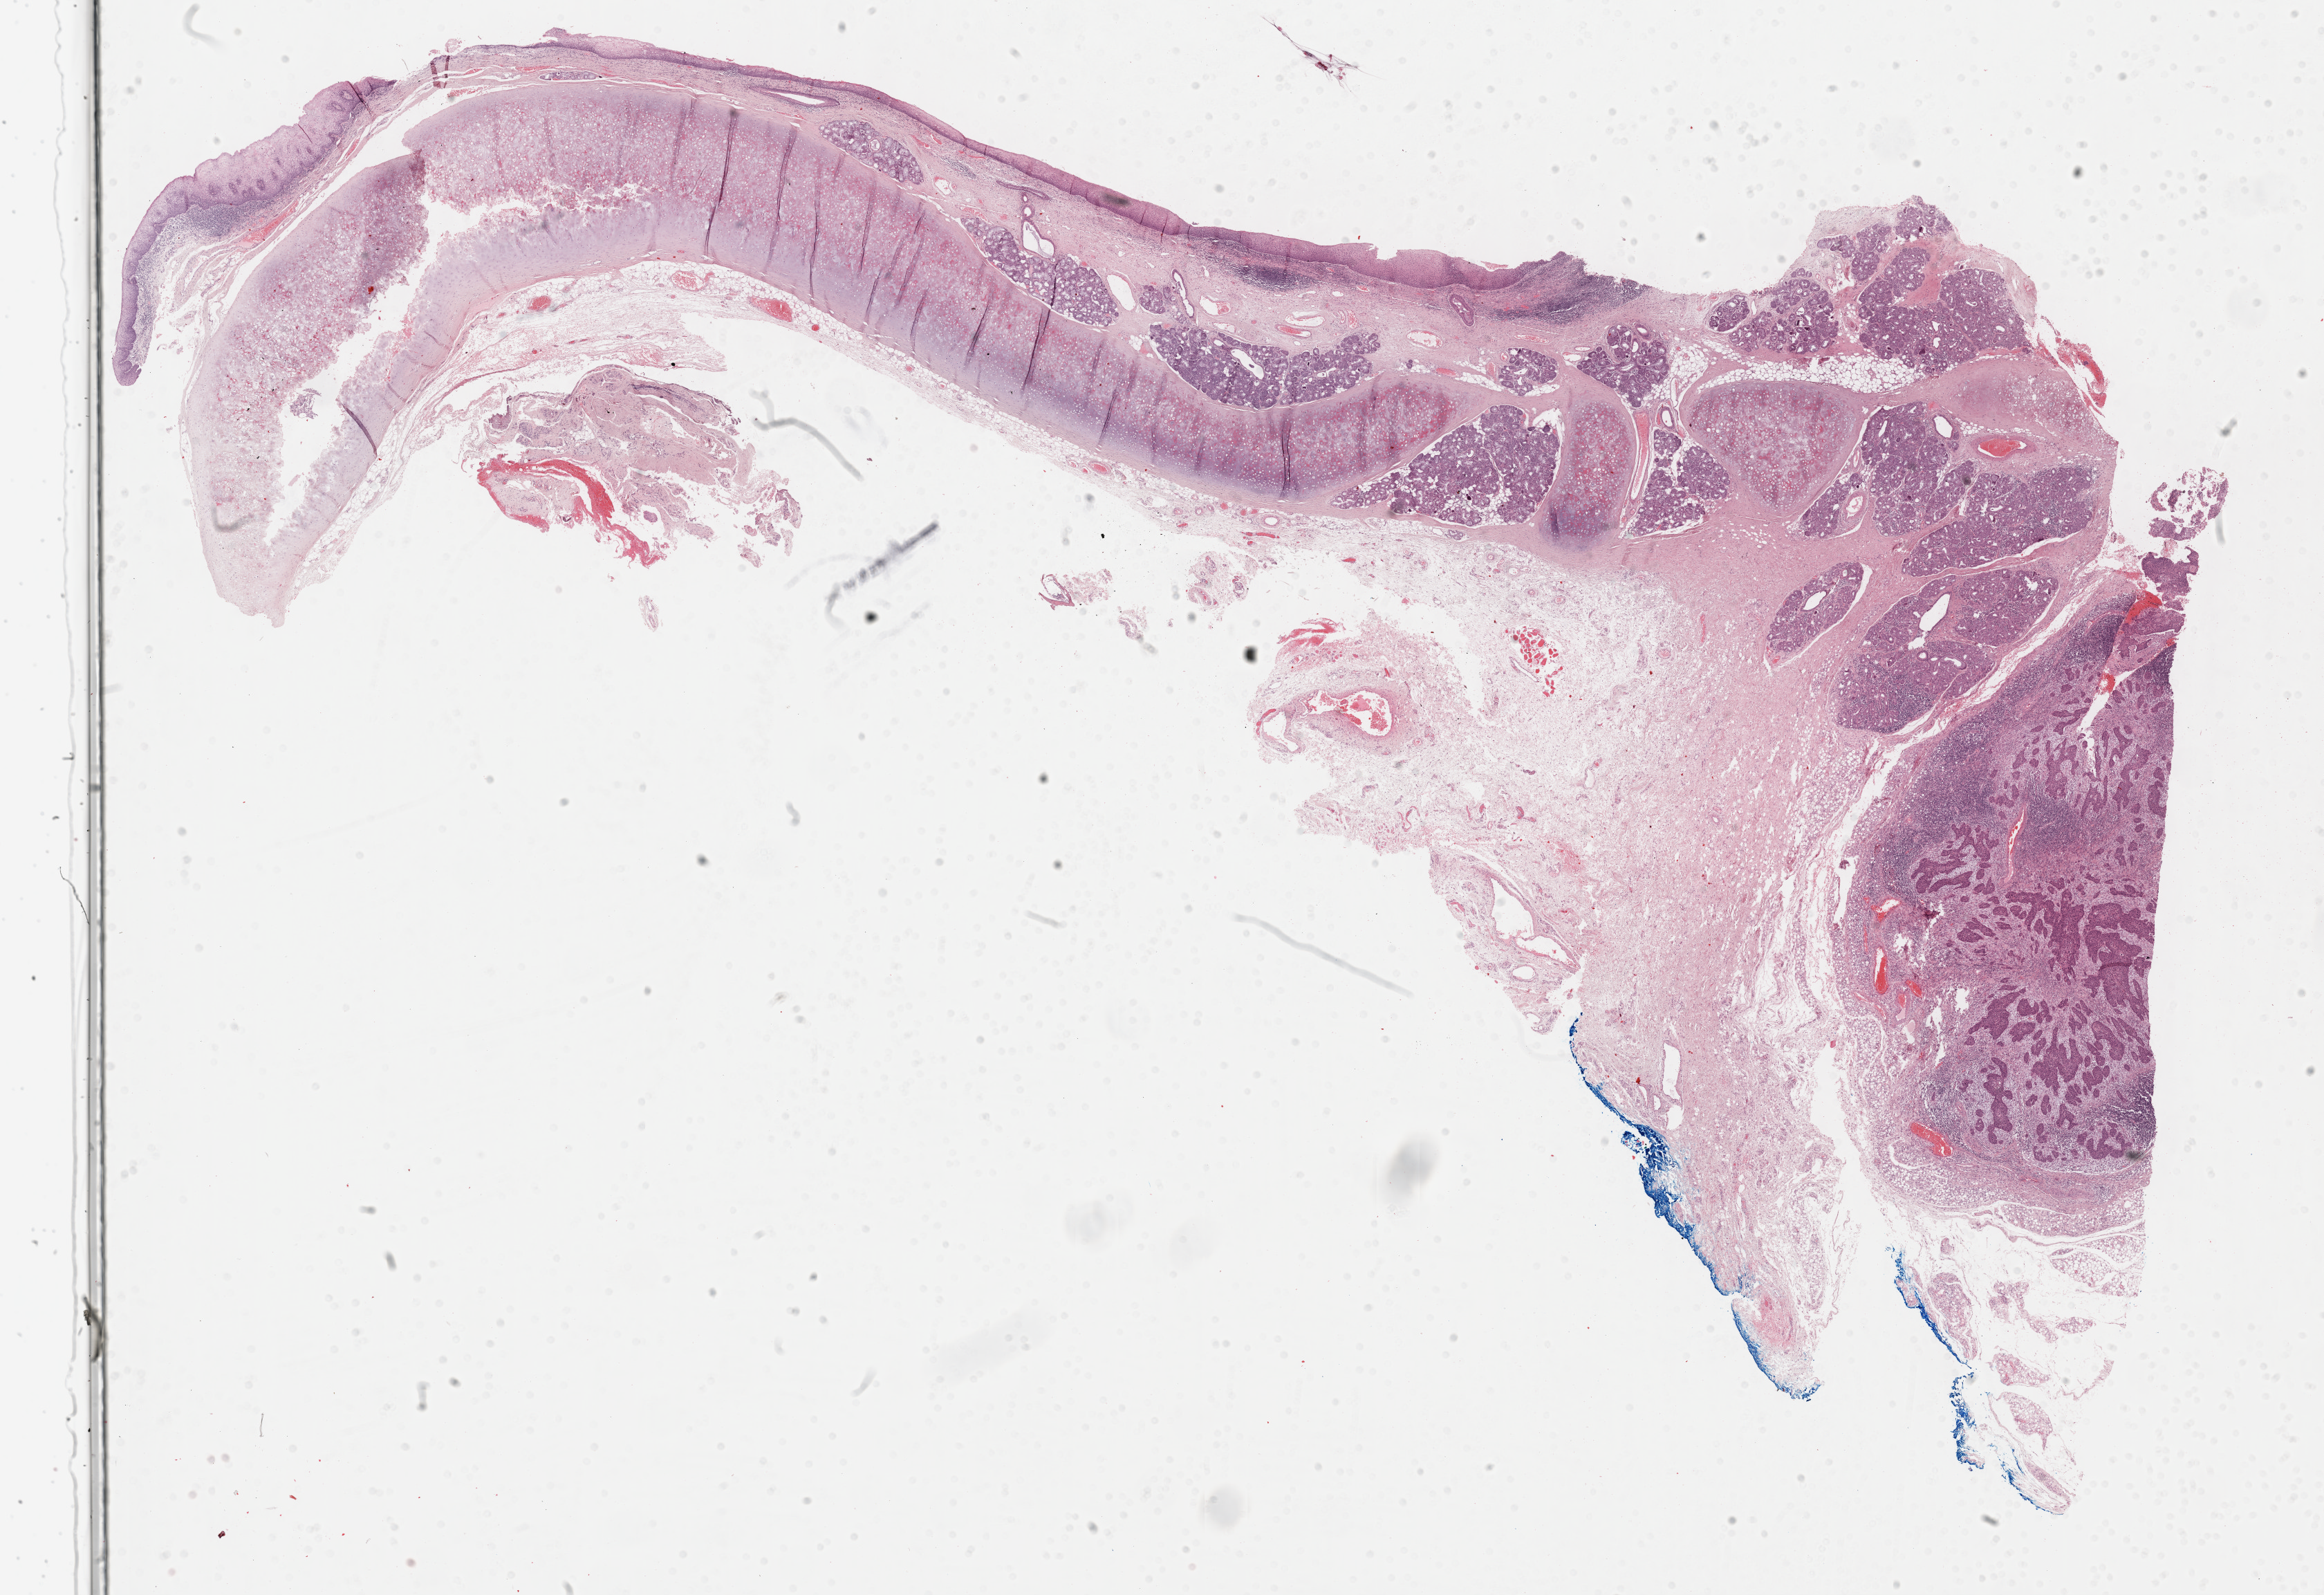
Digitized Hematoxylin and eosin (H&E) stained tissue section (whole slide) — low-resolution overview of the scanned area, about 27.2 x 18.6 mm (slide scanned at 40x); FFPE section; head and neck, primary tumour sample. Patient: male, age at initial diagnosis 67 years. Histologic grade: G3 (poorly differentiated).
AJCC pathologic stage: IVA (7th edition). Diagnosis: Squamous cell carcinoma, keratinizing, NOS (larynx, NOS).